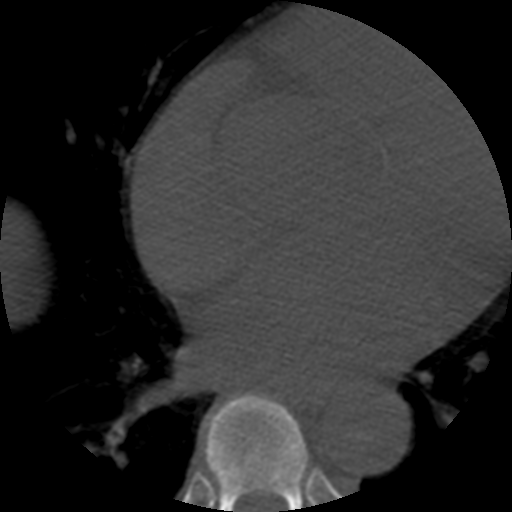
CT including the spine, one axial slice; reconstruction kernel STANDARD; bone window (W 1800 / L 400 HU); 512 × 512 image matrix, field of view 160 × 160 mm. Patient age 57 years. From the clinical record (not read from this slice): primary cancer: prostate.
Structures marked on this image (semi-automatic segmentation, software-assisted and operator-edited):
- T7 vertebra: bounding box (x1, y1, x2, y2) in pixels: (204, 393, 310, 512)